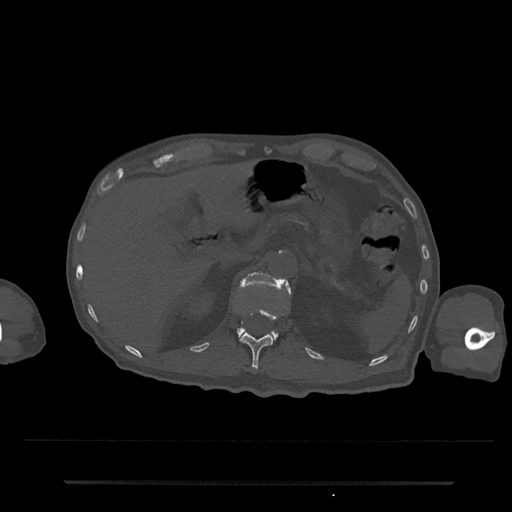
CT including the spine, one axial slice. Slice 174 of 797 in the series (ordered by position). Reconstruction kernel Br40s/3. 120 kVp. Bone window (W 1800 / L 400 HU). 512 × 512 image matrix, field of view 427 × 427 mm. Patient: male, 74 years. From the clinical record (not read from this slice): primary cancer: prostate.
Annotated regions visible in this slice (semi-automatic segmentation, software-assisted and operator-edited):
- L1 vertebra: bounding box <237,271,291,338> (left, top, right, bottom; pixels)
- T12 vertebra: <240,308,278,371>